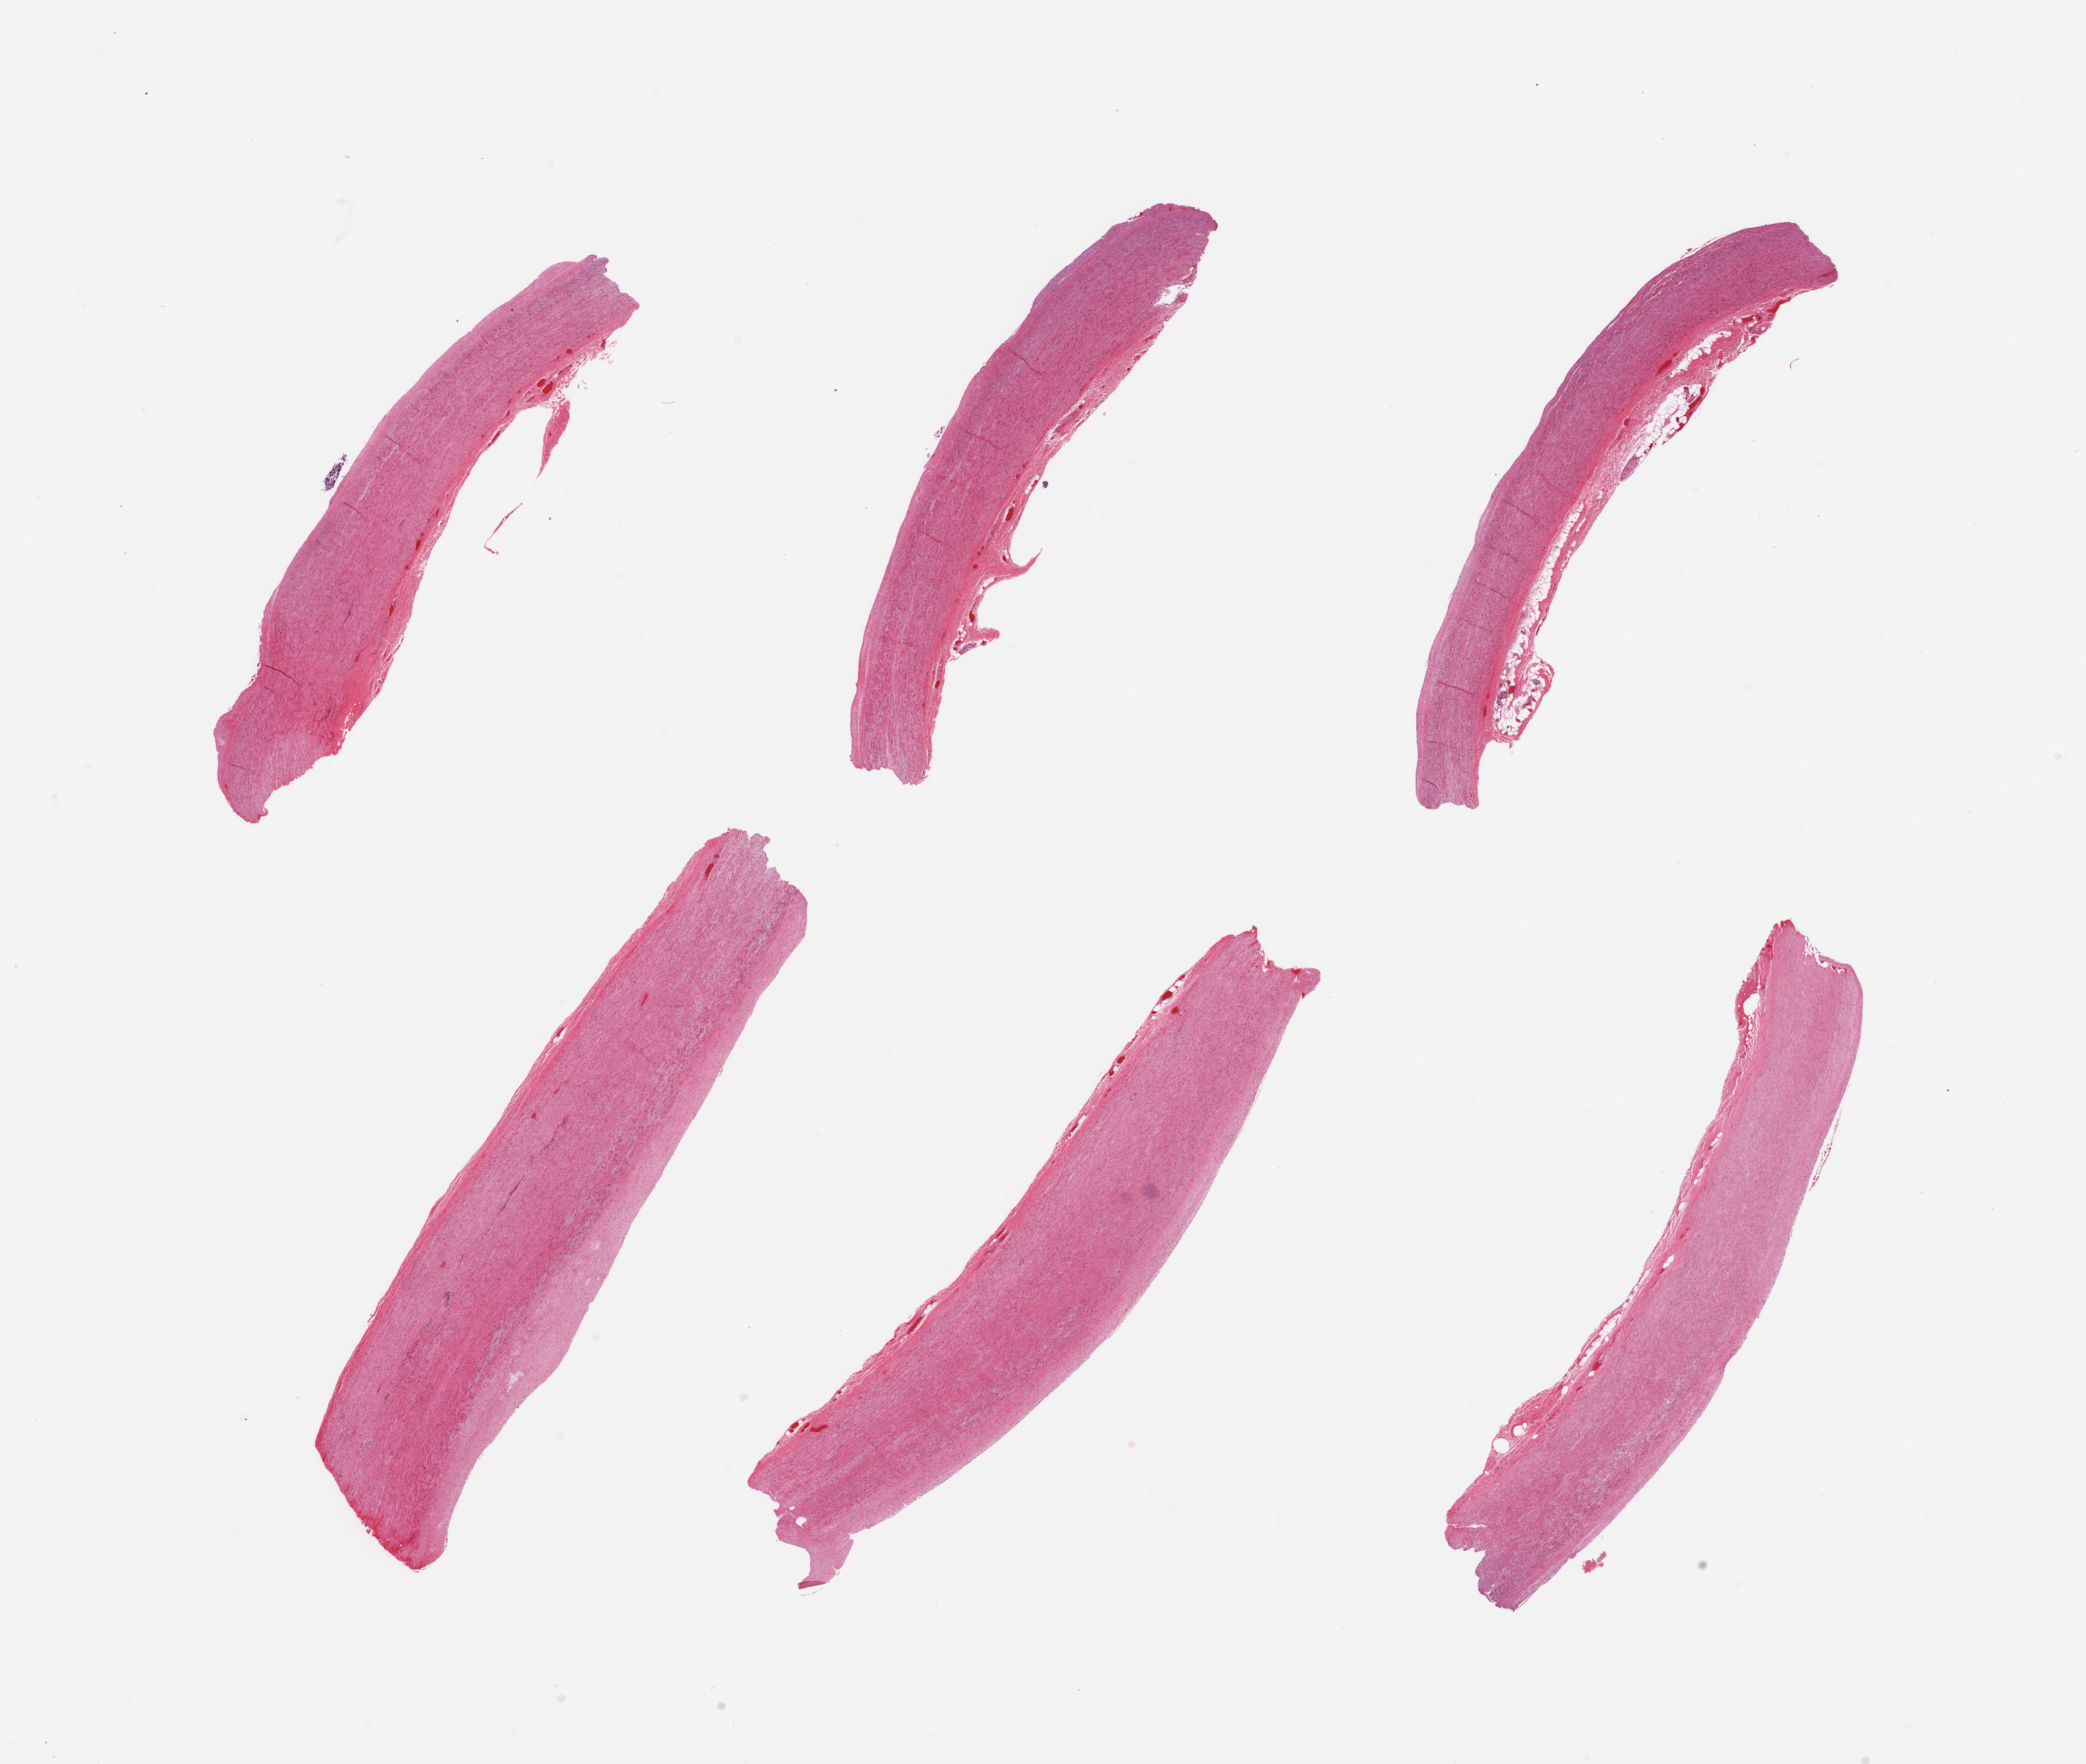
Whole-slide image, H&E stain, shown as a low-resolution overview of the whole scanned area (about 24.6 x 20.8 mm); PAXgene-fixed, paraffin-embedded tissue; target tissue: aorta; tissue donor sample. Male donor.
Review note (as recorded): 6 pieces; atherosis layer up to 0.6mm and attached congested adventitia.